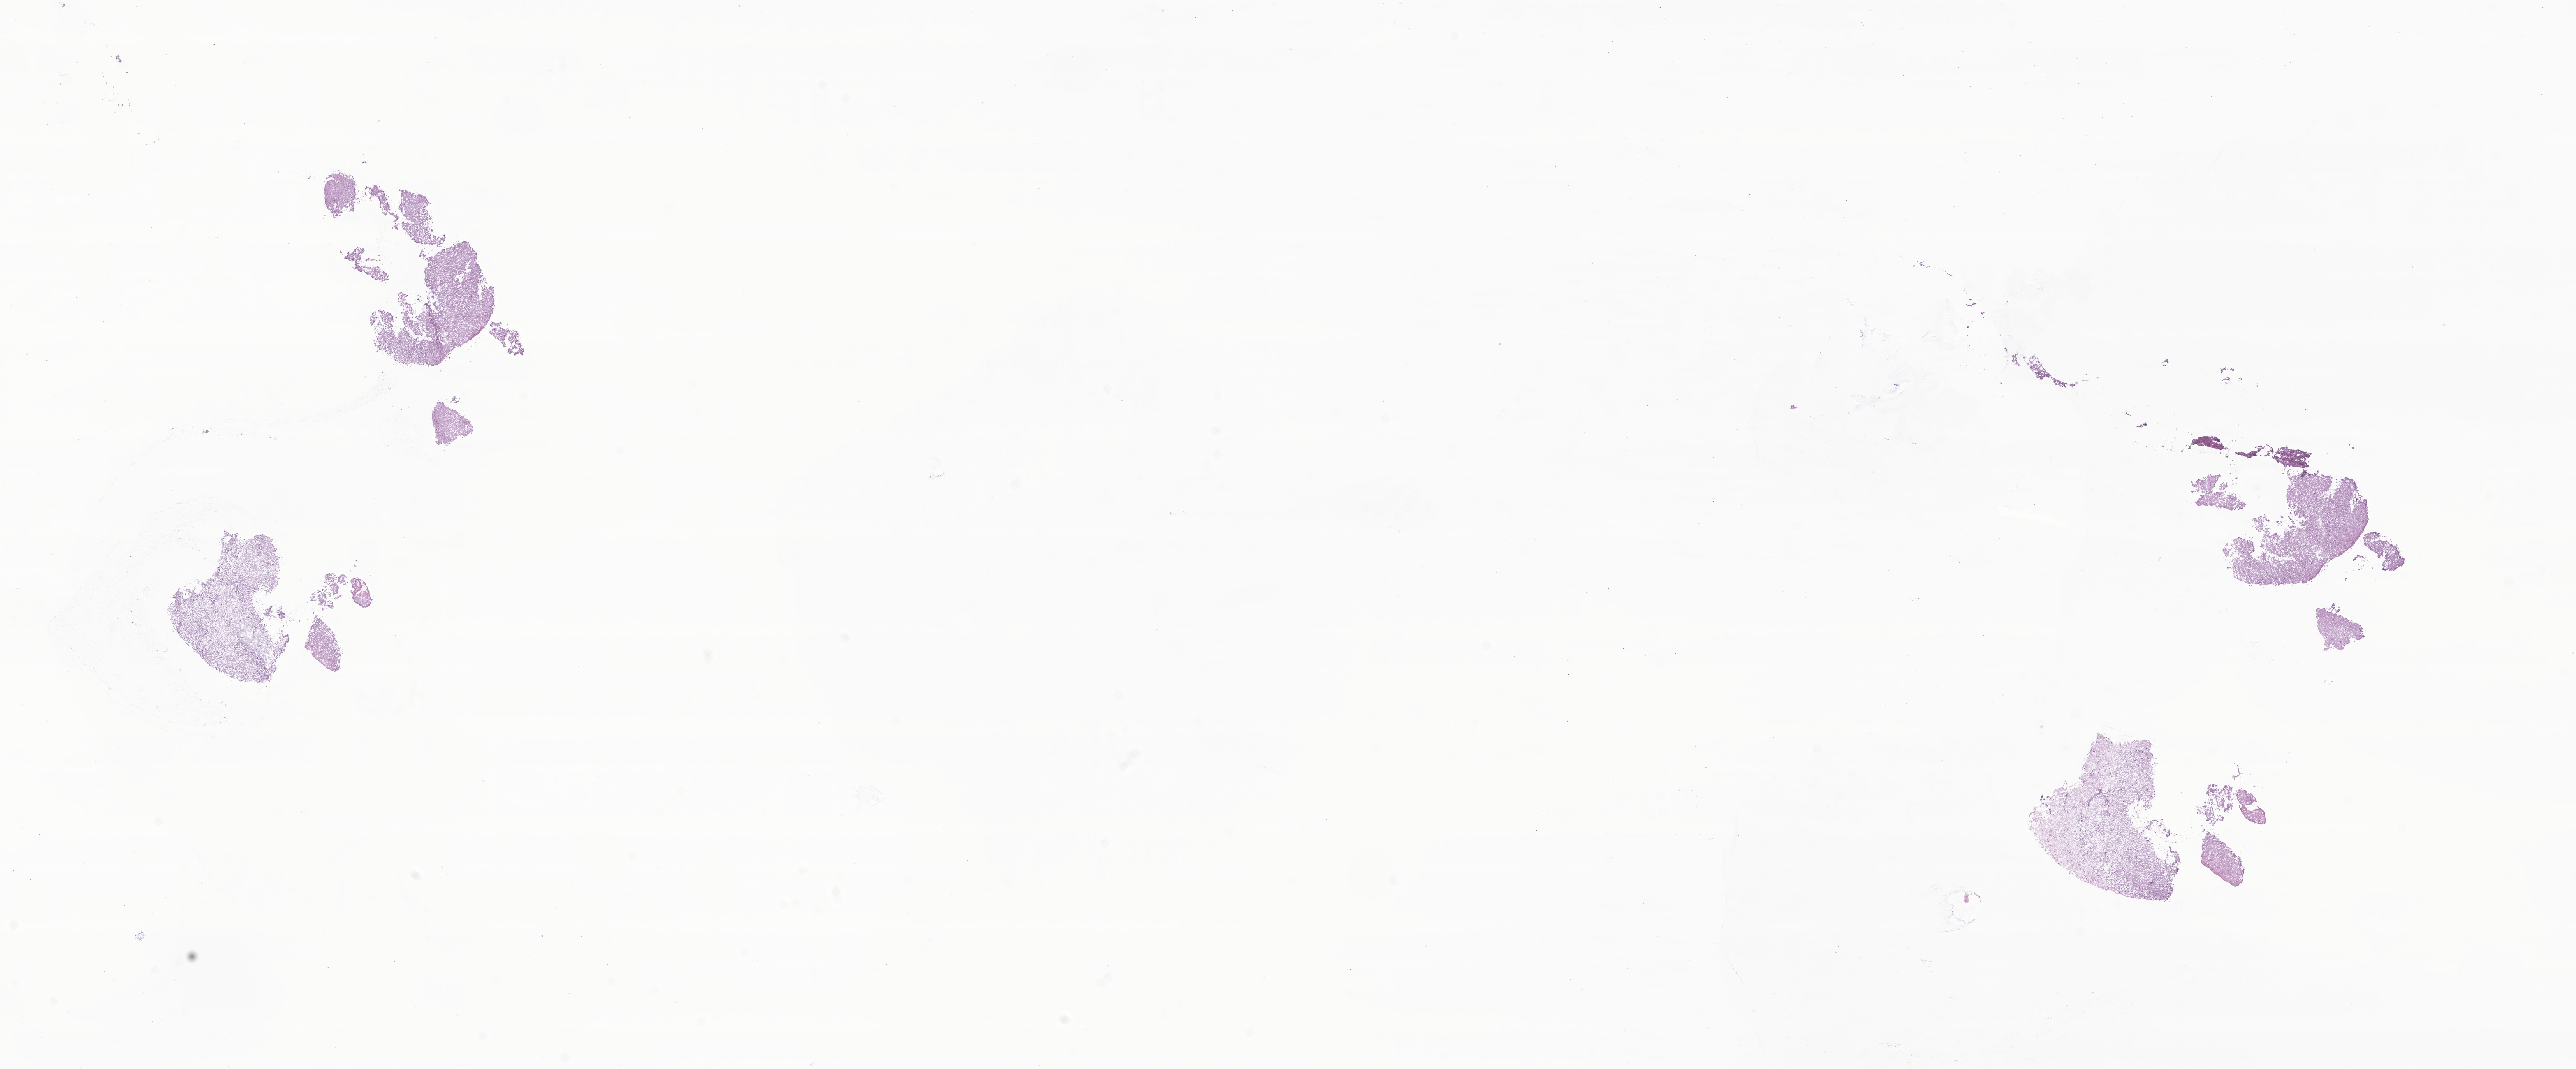
Haematoxylin and eosin whole-slide image of tumor tissue from the brain, whole scanned area (about 27.9 x 11.6 mm) shown as a low-resolution overview; frozen section (OCT-embedded). Patient female; age 134 months (11 years 2 months).
Diagnosis (ICD-O-3 morphology term): Ganglioglioma, NOS.